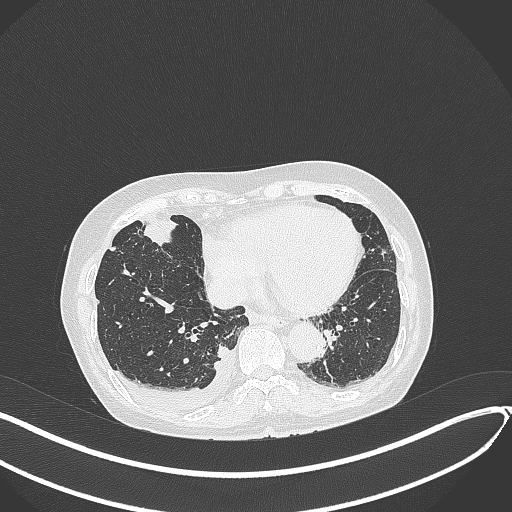
Chest CT, one axial slice. Position 119 of 418 along the scan axis. Lung window (W 1500 / L -600 HU). 1 mm slice thickness. 512 × 512 image matrix, field of view 400 × 400 mm. Female patient, age 75 years. From the clinical record (not read from this slice): clinical TNM (as recorded): T2a N3 M0.
Structures marked on this image (rectangle marked by the reading radiologist):
- lung tumour (recorded histology: adenocarcinoma): bounding box <136,214,190,253> (left, top, right, bottom; pixels)